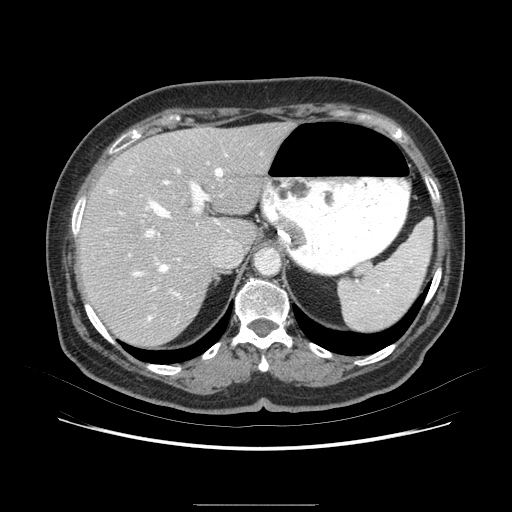
Contrast-enhanced abdominal CT (liver protocol), one axial slice; position 54 of 79 along the scan axis; 120 kVp; soft-tissue window (W 400 / L 40 HU); 2.5 mm slice thickness; 512 × 512 image matrix, field of view 380 × 380 mm. From the clinical record (not read from this slice): diagnosis: hepatocellular carcinoma (patient treated with transarterial chemoembolisation; whether this scan precedes or follows treatment is not stated here); TNM stage (as recorded): Stage-I; Child-Pugh class: A; tumour differentiation: poorly differentiated; tumour nodularity: uninodular.
Structures marked on this image (semi-automatically segmented with operator editing):
- abdominal aorta: bounding box <256,250,282,277> (left, top, right, bottom; pixels)
- liver parenchyma outside the tumour (the mass and vessels are separate outlines, so this box may not span the whole liver): <76,126,300,338>
- liver vessels: <115,159,244,282>